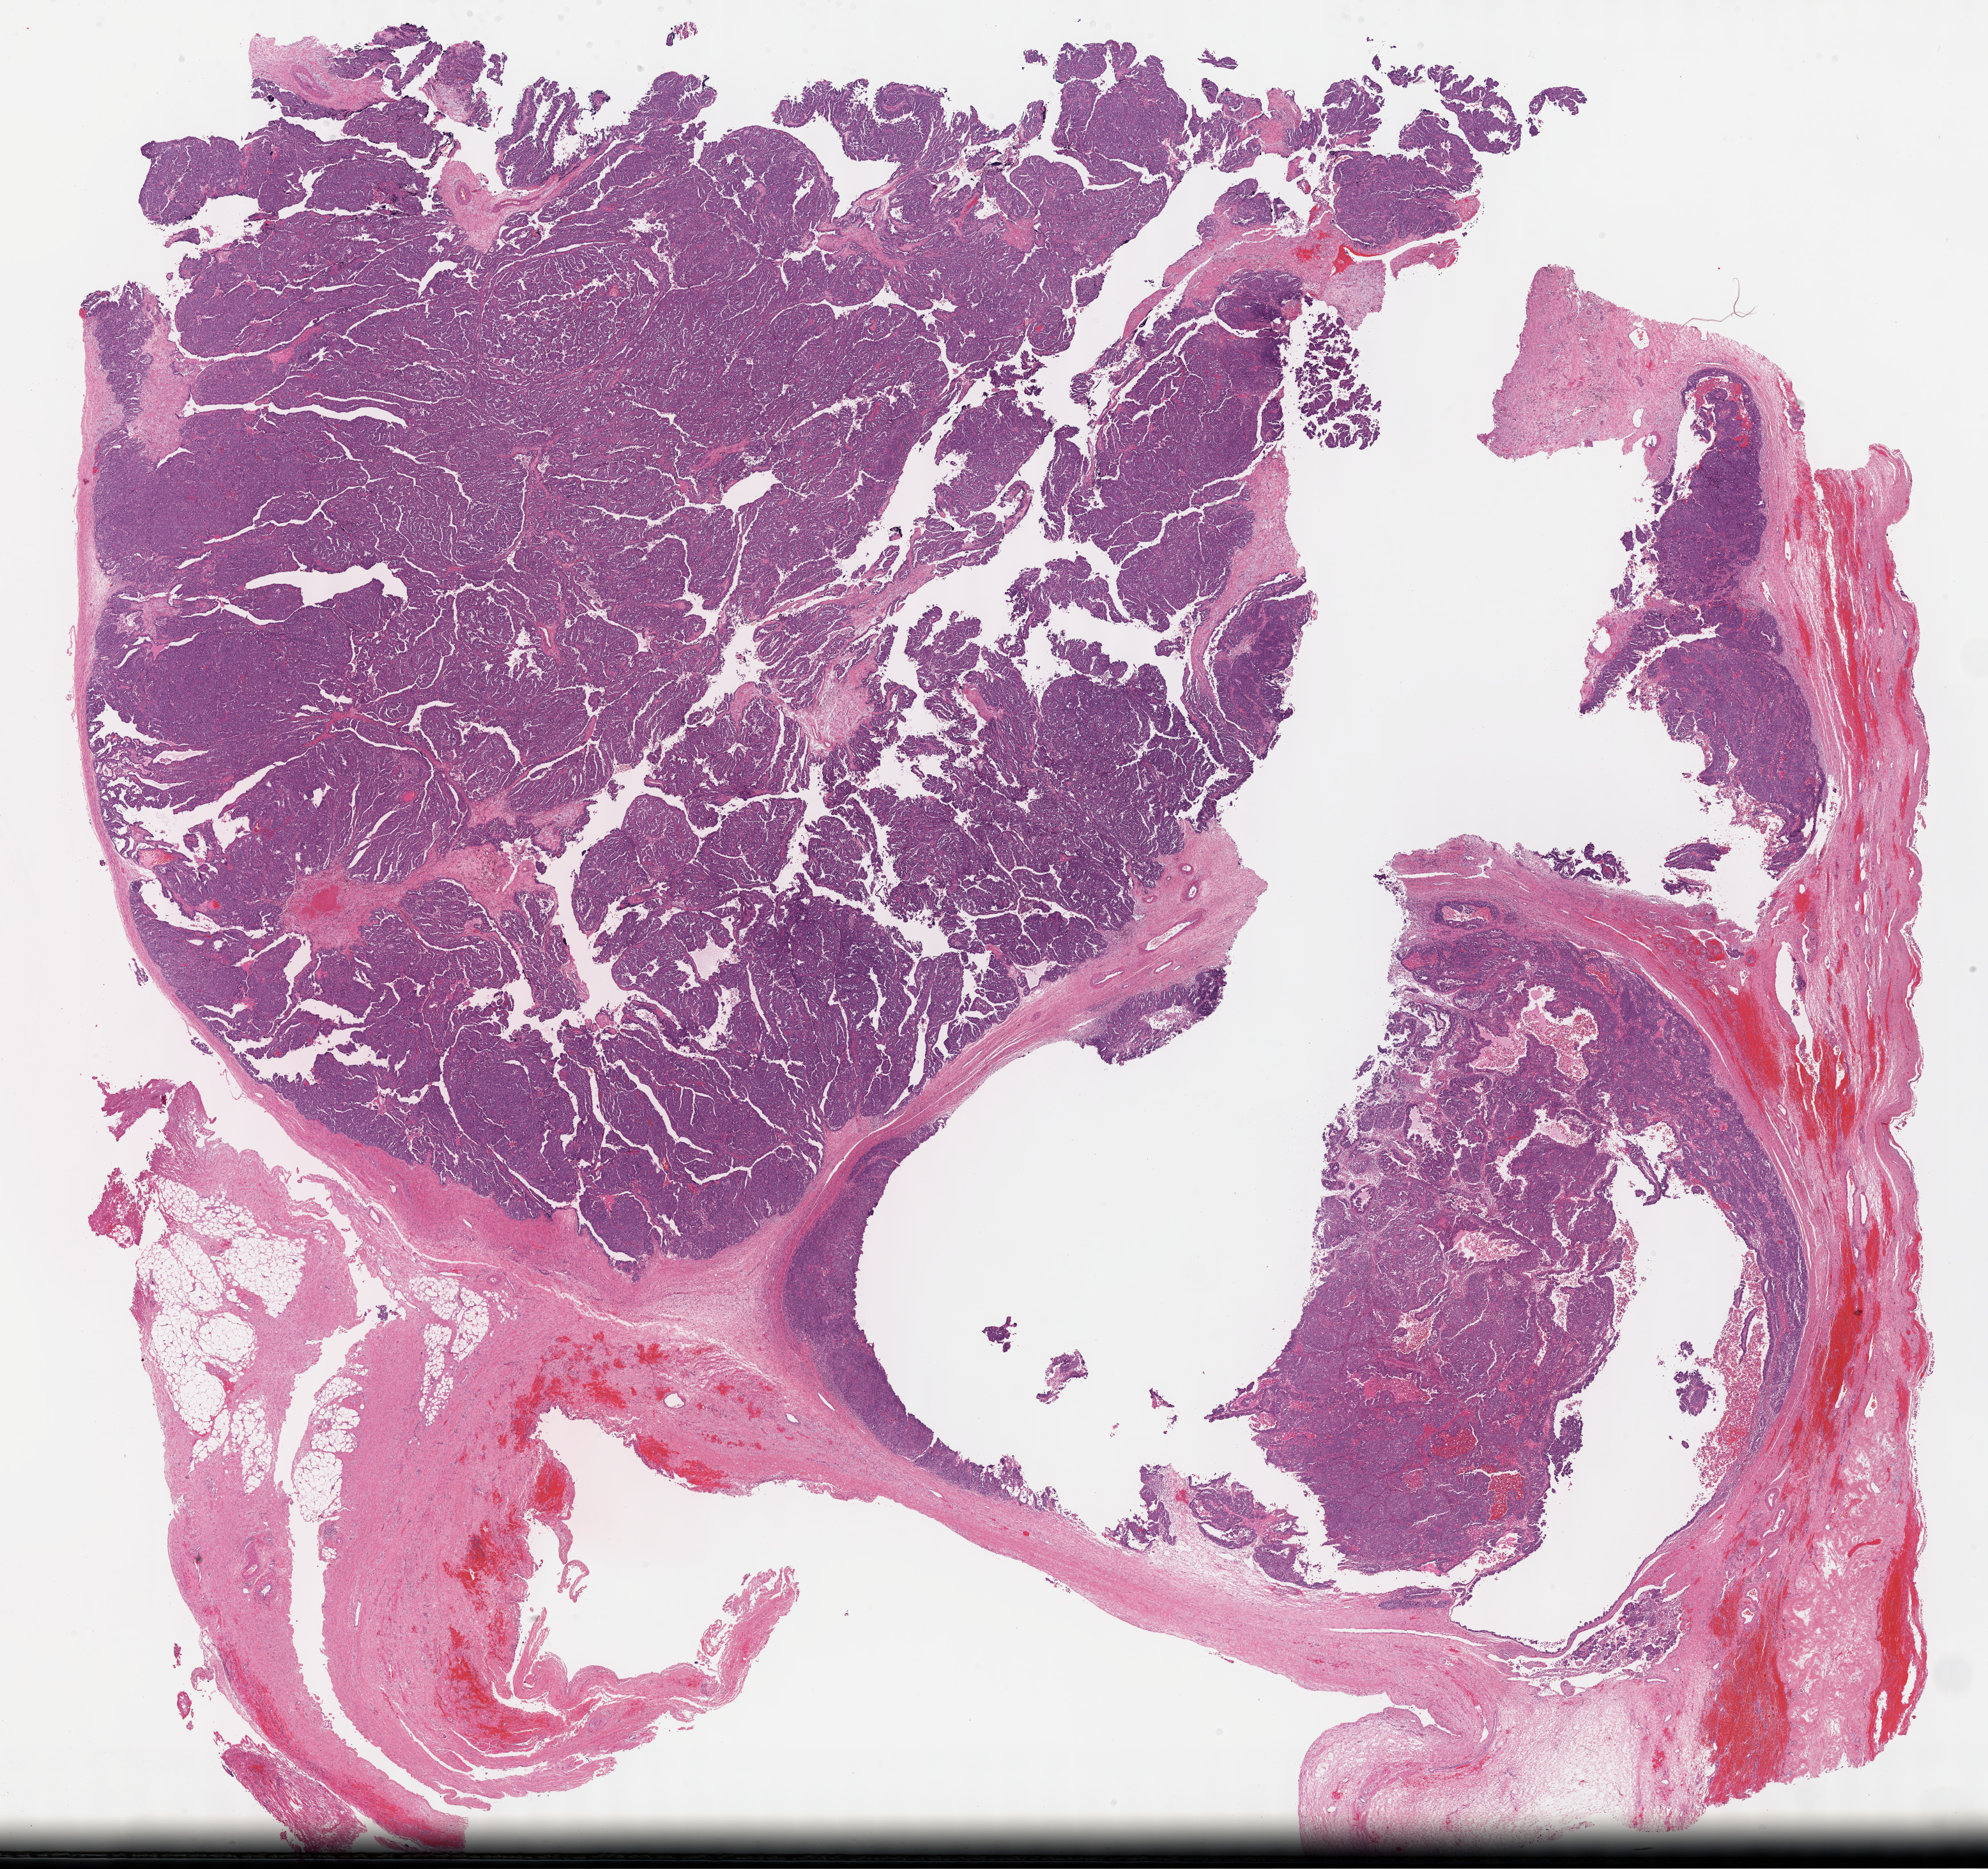
Hematoxylin and eosin (H&E) stained whole-slide image — shown as a low-resolution overview of the whole scanned area (about 25.2 x 23.7 mm). Formalin-fixed paraffin-embedded (FFPE) diagnostic section. Primary tumour sample from the ovary. Female patient; age at initial diagnosis 59 years. Histologic grade: G3 (poorly differentiated).
FIGO stage: IIIC. Diagnosis: Serous cystadenocarcinoma, NOS.